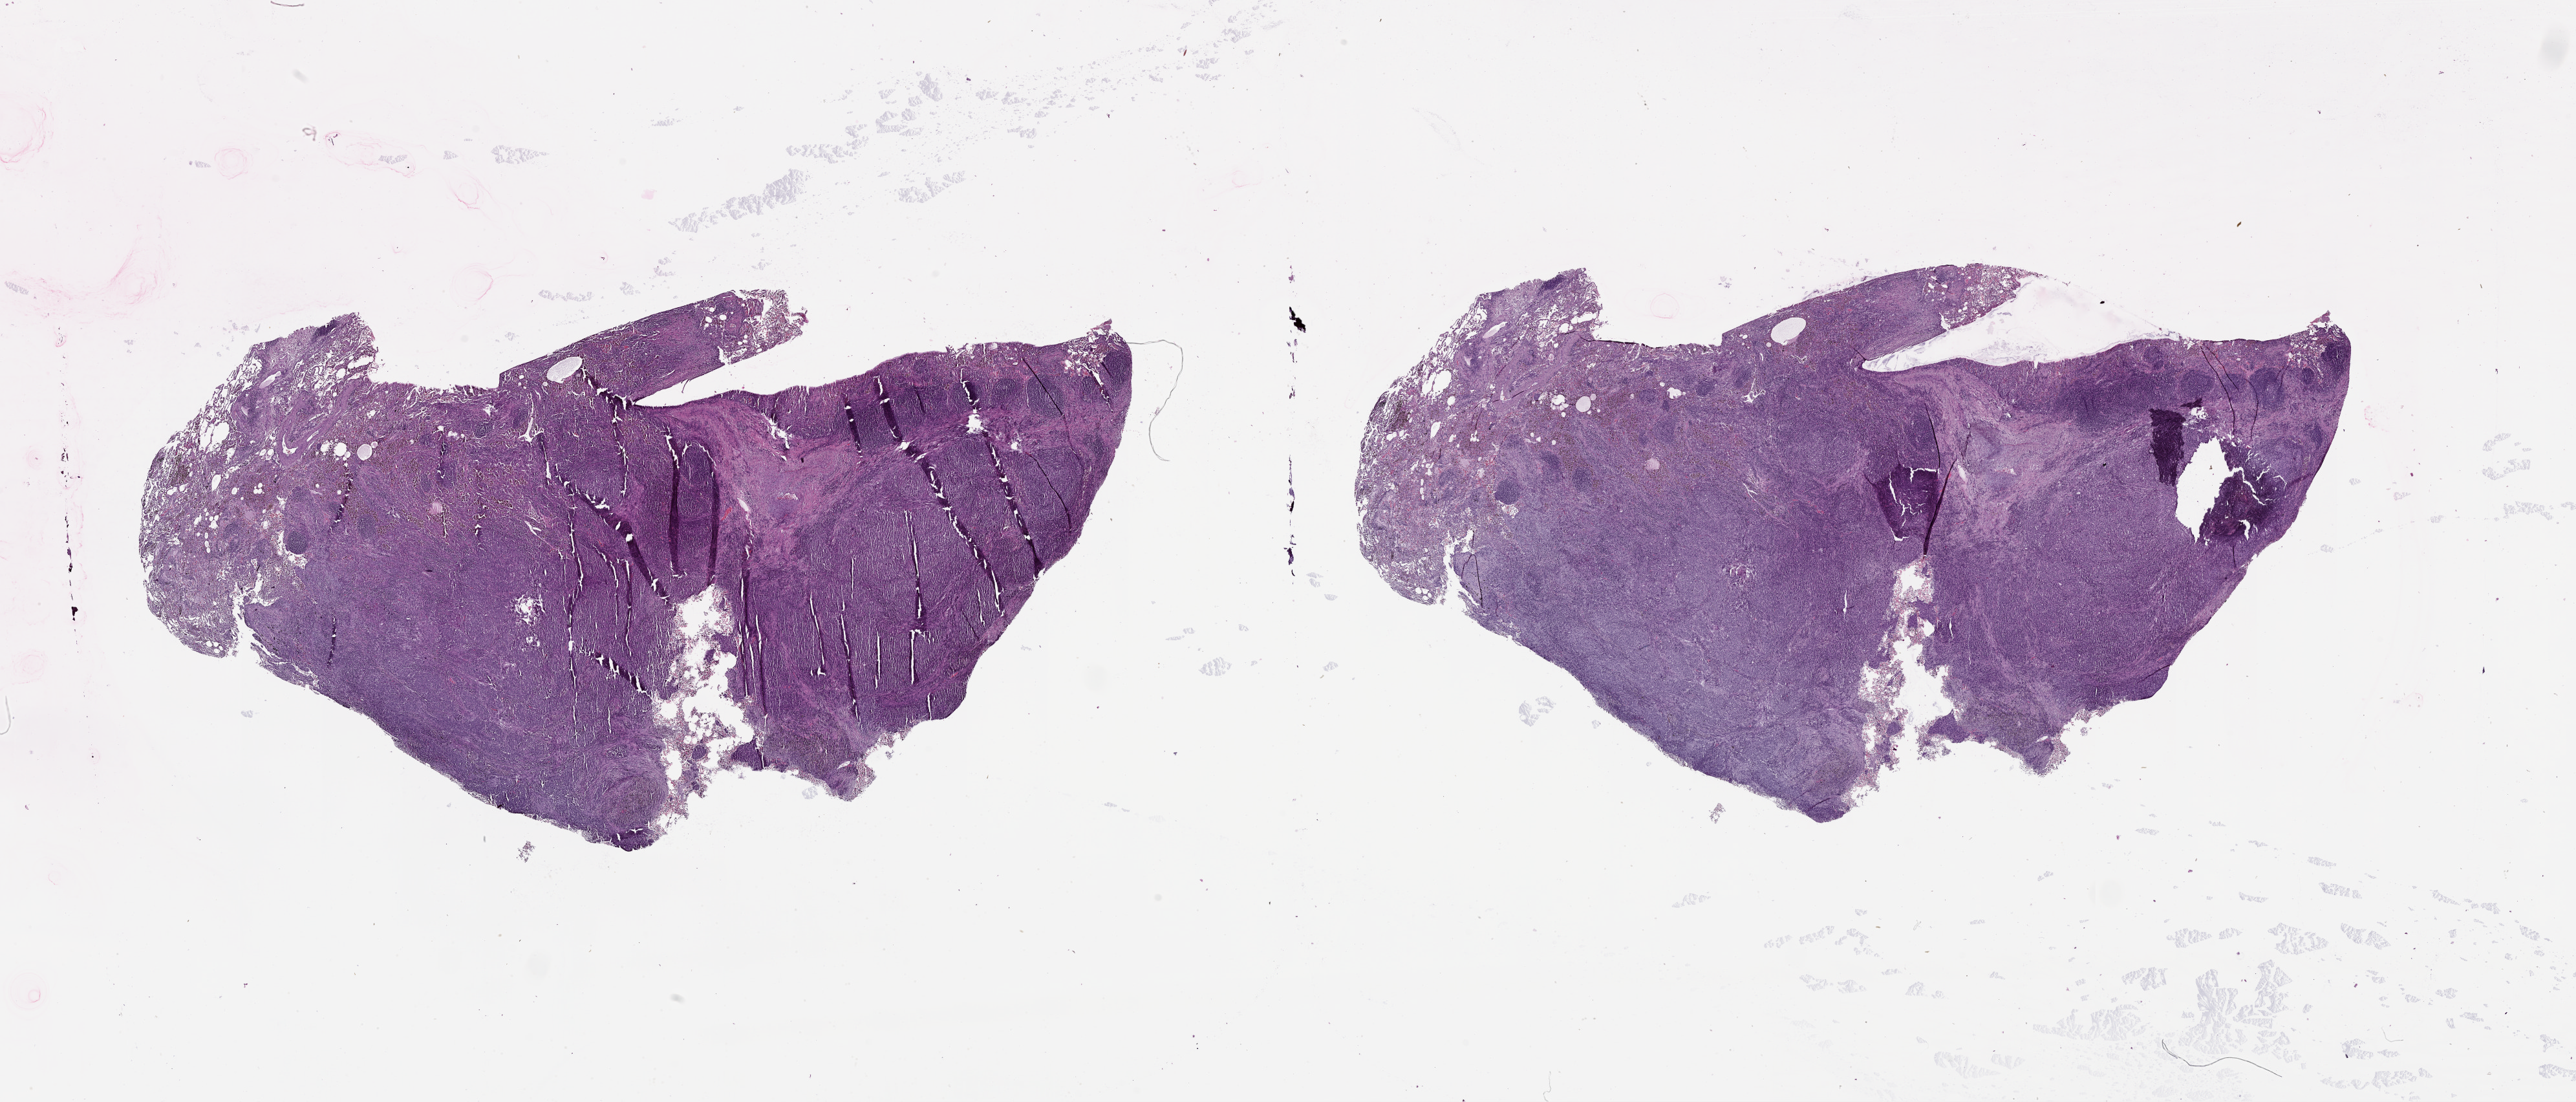
Digitized H&E-stained tissue section (whole slide) — a low-resolution overview of the entire scanned area, about 32.1 x 13.7 mm (slide scanned at 20x). Lung, tumour tissue. Patient: male, age 65 years.
- patient diagnosis (cohort enrolment): squamous cell carcinoma (lung)